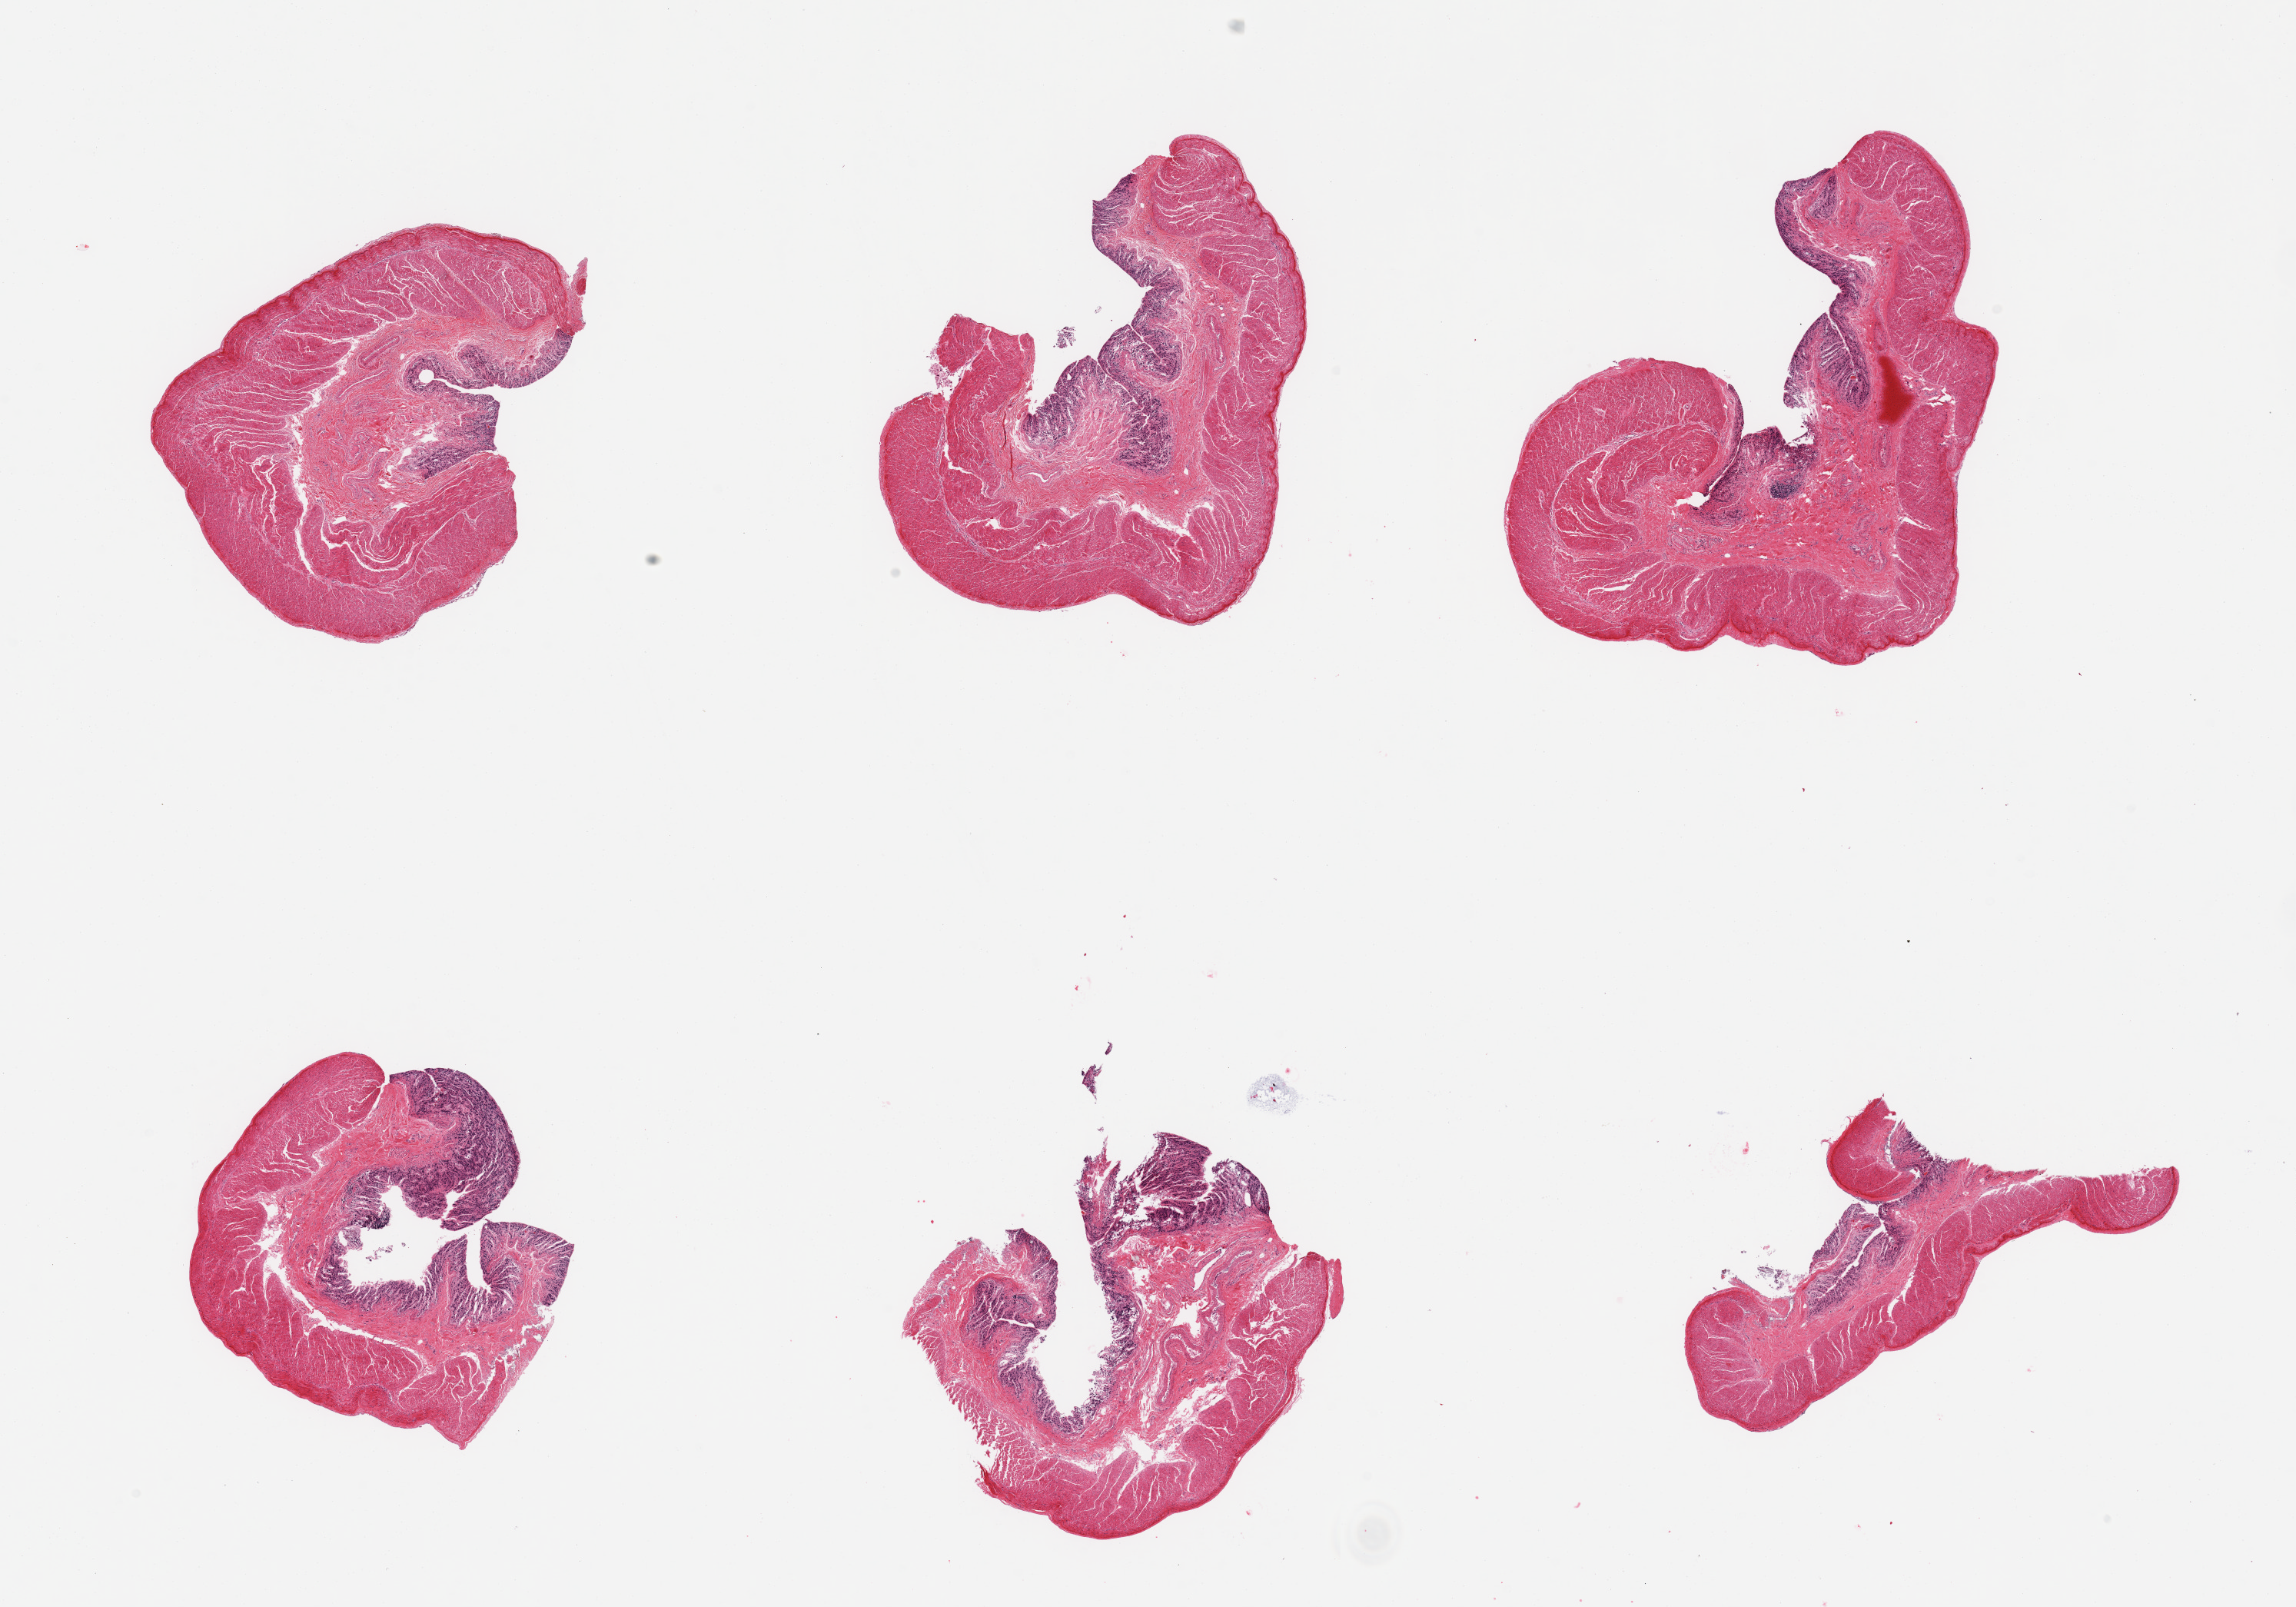
Whole-slide image, hematoxylin and eosin (H&E) stain, shown as a low-resolution overview of the whole scanned area (about 23.6 x 16.5 mm, slide scanned at 20x), PAXgene-fixed, paraffin-embedded tissue, target tissue: transverse colon, tissue donor sample. Donor: male.
* pathologist's review note for this sample: 6 pieces; autolyzed mucosa, intact muscle